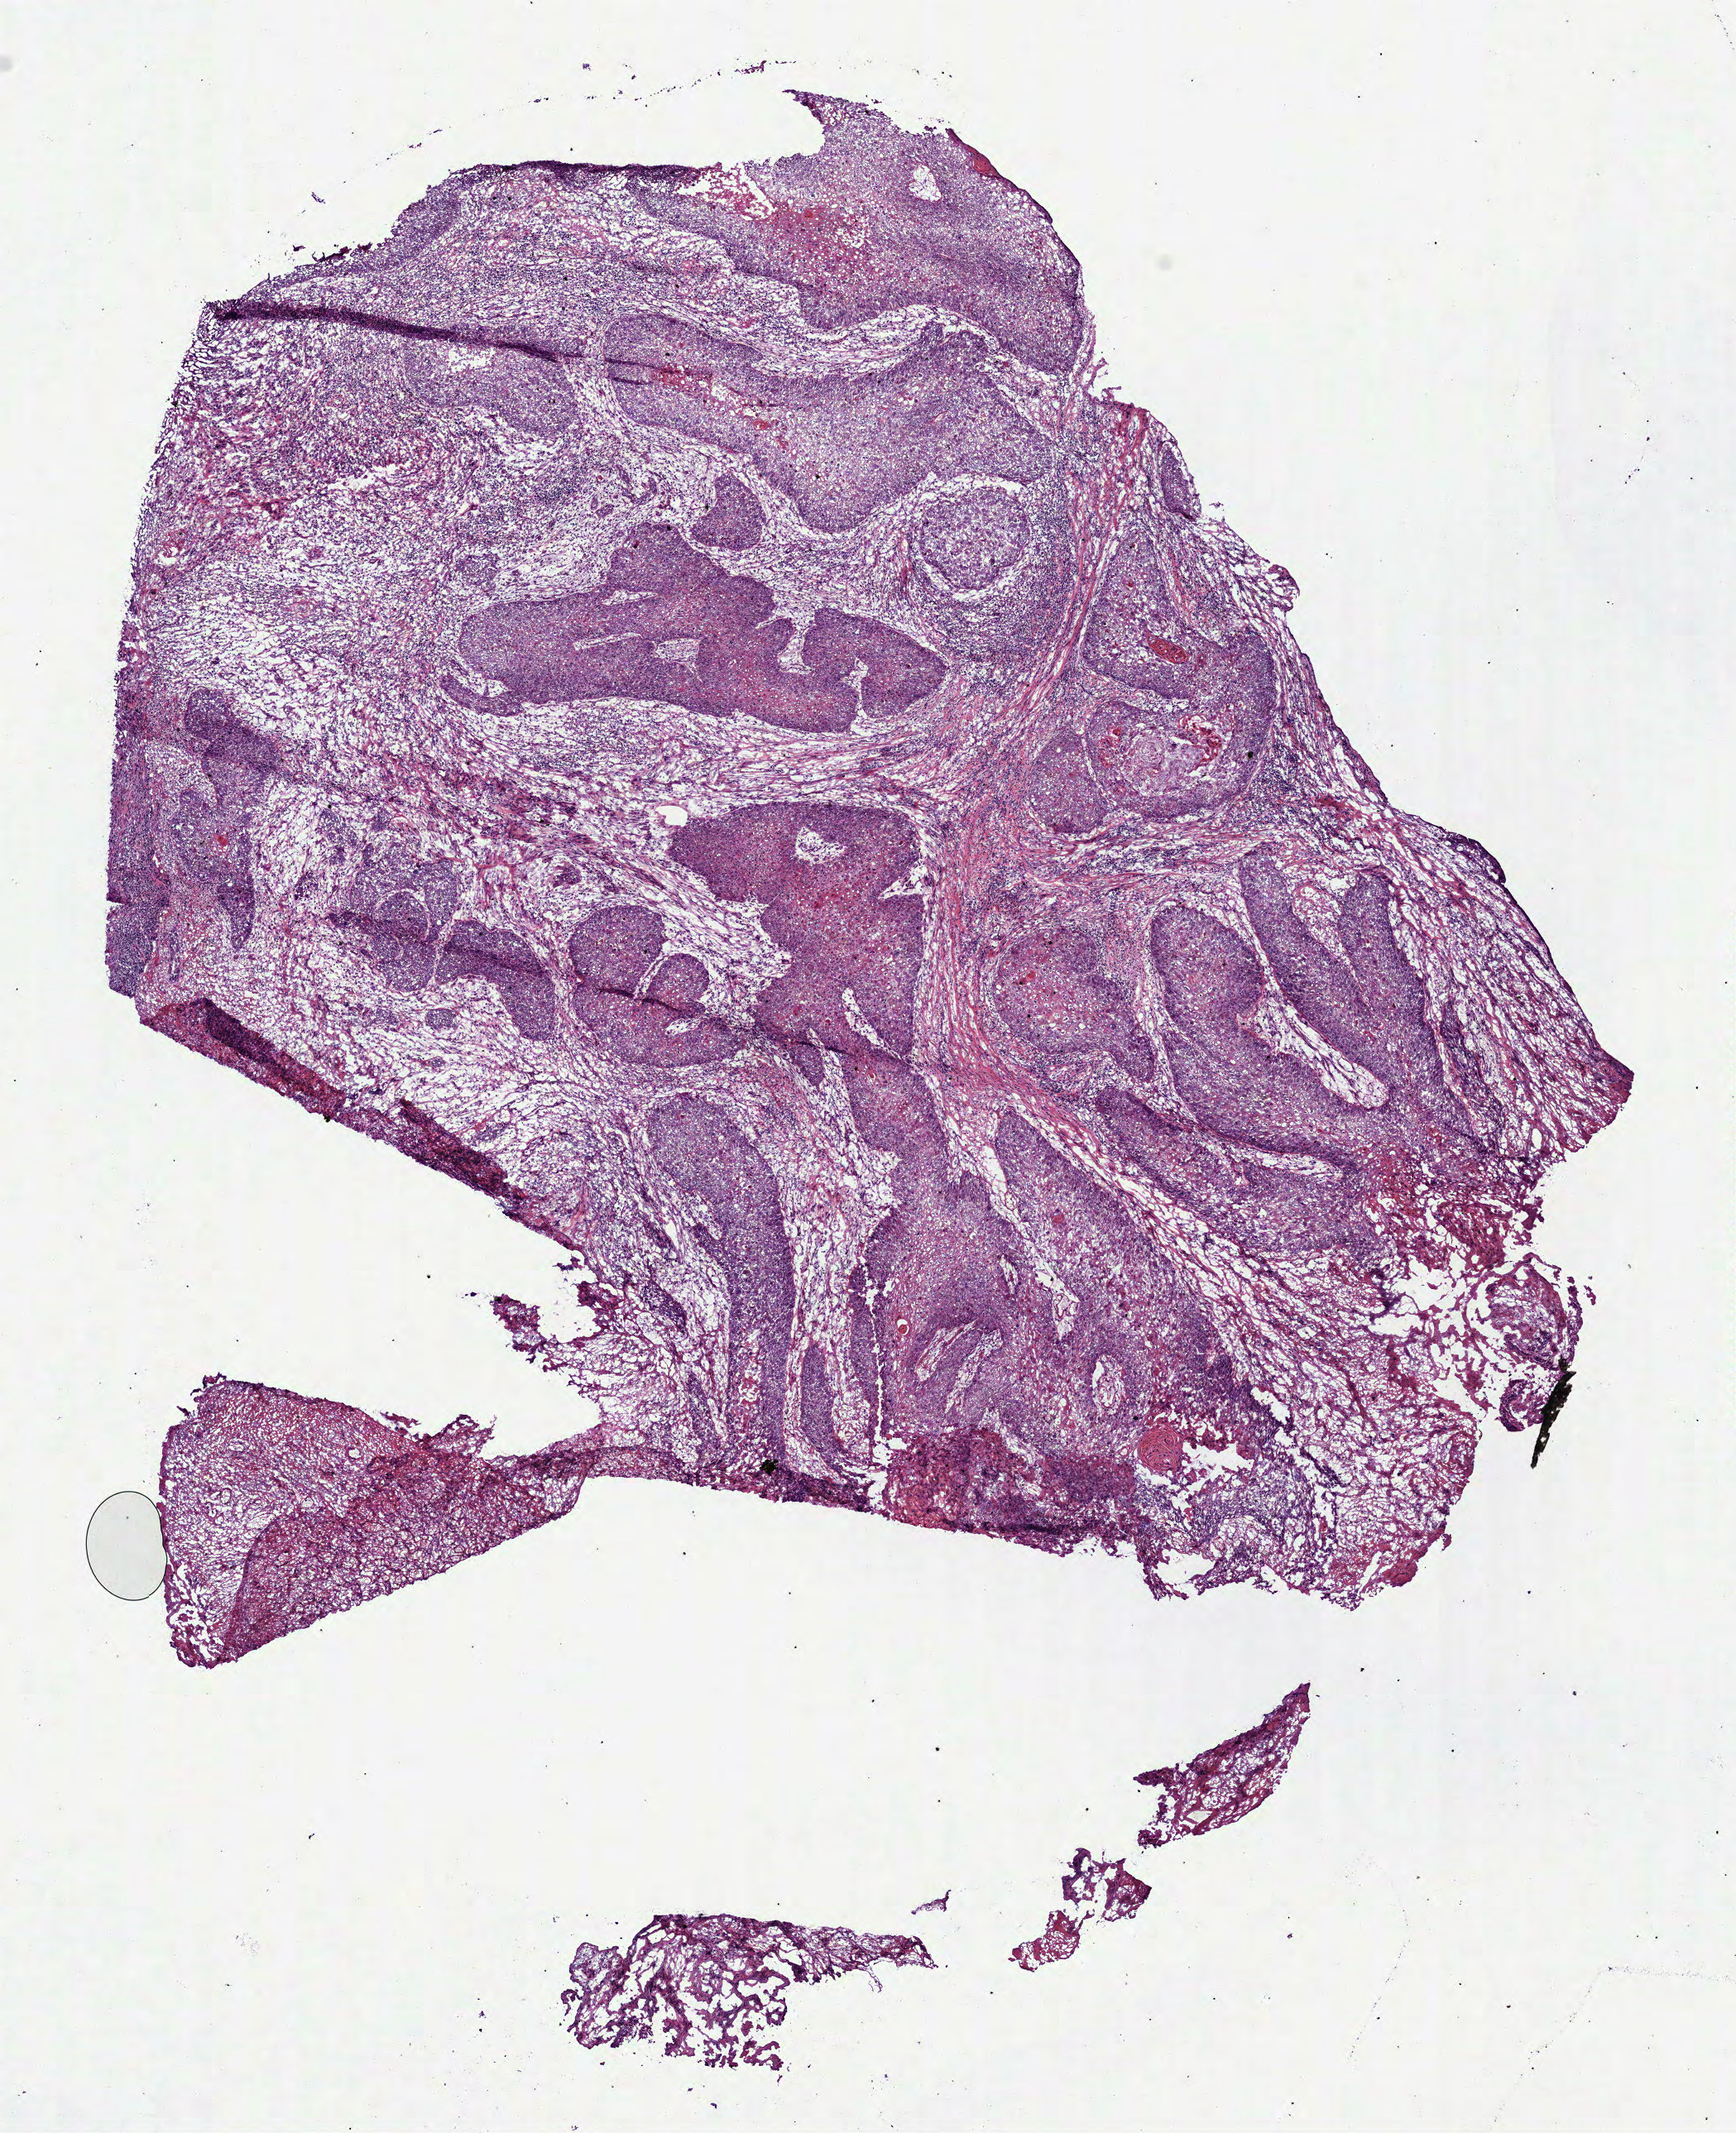
Whole-slide histology image, Hematoxylin and eosin (H&E) stained, shown as a low-resolution overview of the whole scanned area (about 8.5 x 10.4 mm, slide scanned at 40x); frozen section; primary tumour sample from the head and neck. Female, age 85 years at initial diagnosis. Histologic grade: G2 (moderately differentiated). Slide review estimates, as recorded: tumour cells 68%, tumour nuclei 65%, normal cells 0%, stromal cells 30%, necrosis 2%.
* AJCC pathologic stage: IVA (7th edition)
* pathologic diagnosis: Squamous cell carcinoma, NOS (overlapping lesion of lip, oral cavity and pharynx)